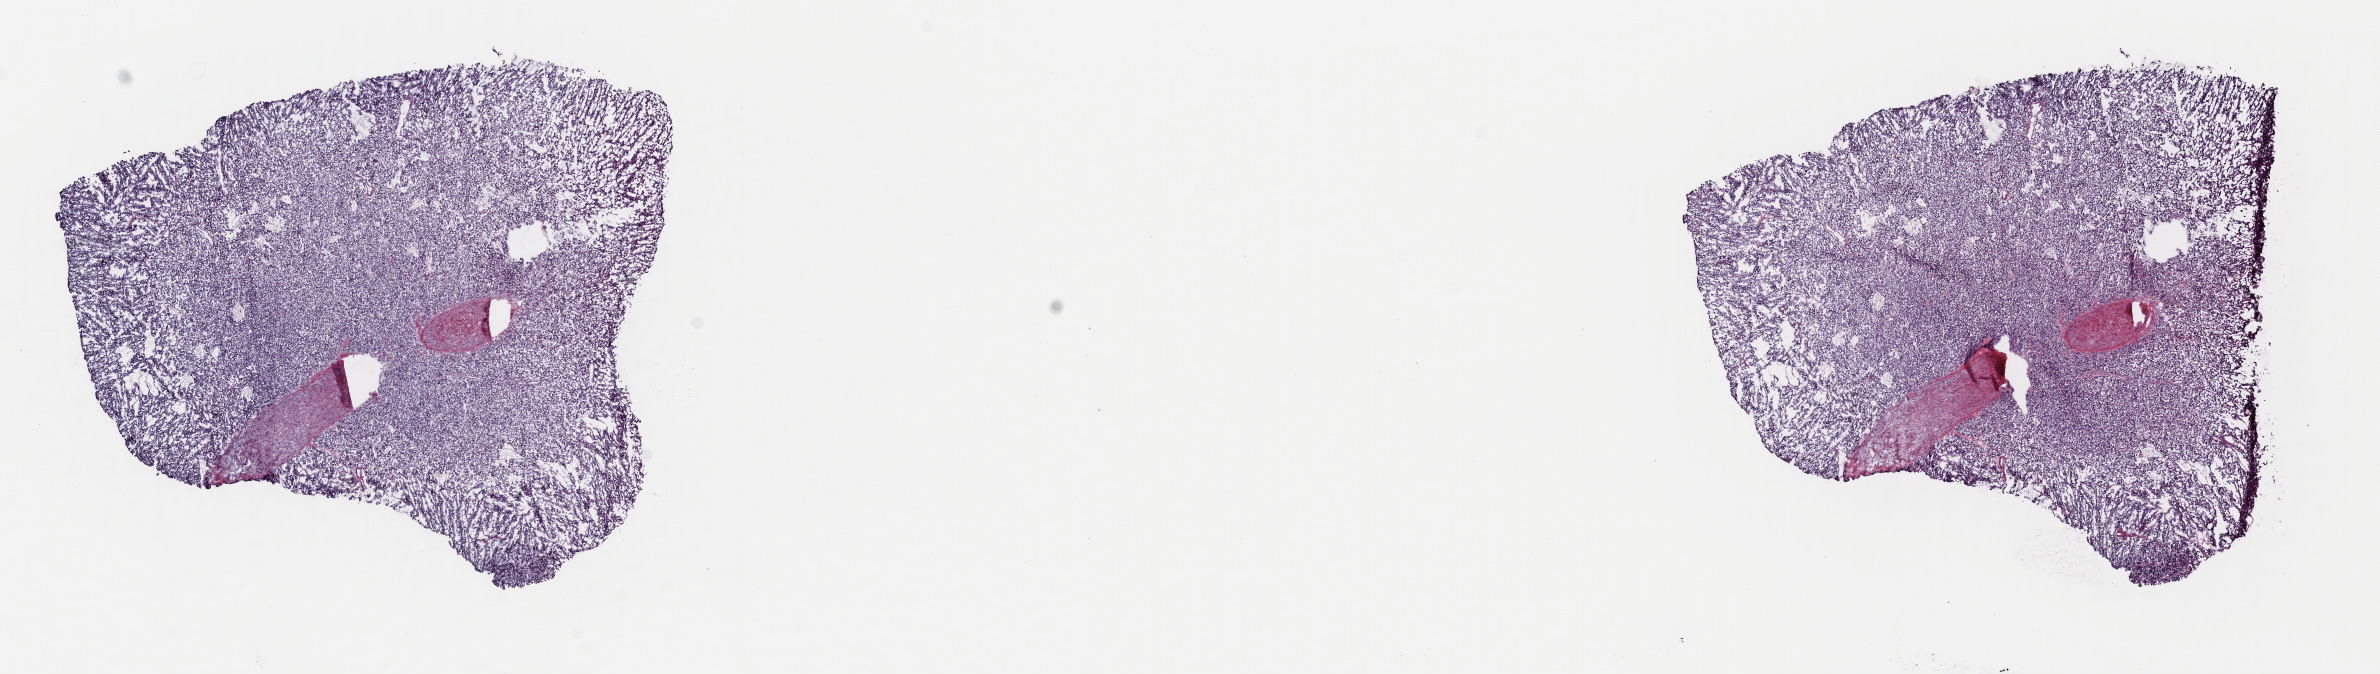
H&E whole-slide image, shown as a low-resolution overview of the whole scanned area (about 18.8 x 5.3 mm), frozen section from the top of the tissue portion, sample: primary tumour, retroperitoneum and peritoneum. Patient: female, age at initial diagnosis 46 years. Composition of this section per pathologist review: tumour cells 95%, tumour nuclei 80%, normal cells 5%, stromal cells 0%, necrosis 0%. Infiltration values recorded for this section: lymphocyte infiltration 1%, monocyte infiltration 0%, neutrophil infiltration 0%.
Diagnosis: Paraganglioma, NOS.